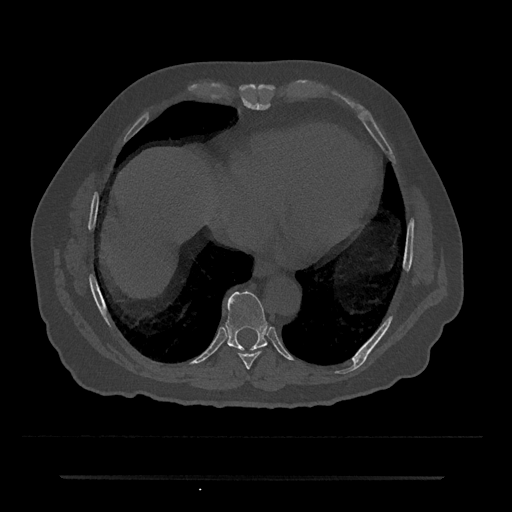
CT including the spine, one axial slice; position 302 of 797 along the scan axis; 120 kVp; bone window (W 1800 / L 400 HU); 512 × 512 image matrix, field of view 437 × 437 mm. Patient: male, 69 years. From the clinical record (not read from this slice): primary cancer: prostate.
Outlined on this slice (semi-automatic segmentation, software-assisted and operator-edited):
- T8 vertebra: bounding box <239,346,265,369> (left, top, right, bottom; pixels)
- T9 vertebra: <225,291,268,351>